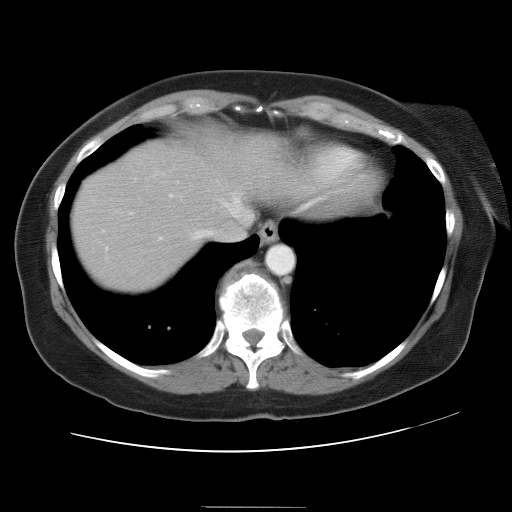
Contrast-enhanced abdominal CT, one axial slice. Slice 28 of 30 in the series (ordered by position). 120 kVp. Soft-tissue window (W 400 / L 40 HU). 7.5 mm slice thickness. 512 × 512 image matrix. Female patient, age 52 years. From the clinical record (not read from this slice): diagnosis: colorectal cancer liver metastases, imaged before liver resection; multiple liver metastases: no; largest metastasis: 3 cm.
Outlined on this slice (expert manual segmentation):
- hepatic veins: bounding box <196,231,211,238> (left, top, right, bottom; pixels)
- liver: <70,134,309,294>
- planned liver remnant (the part of the liver to remain after resection): <178,134,309,208>